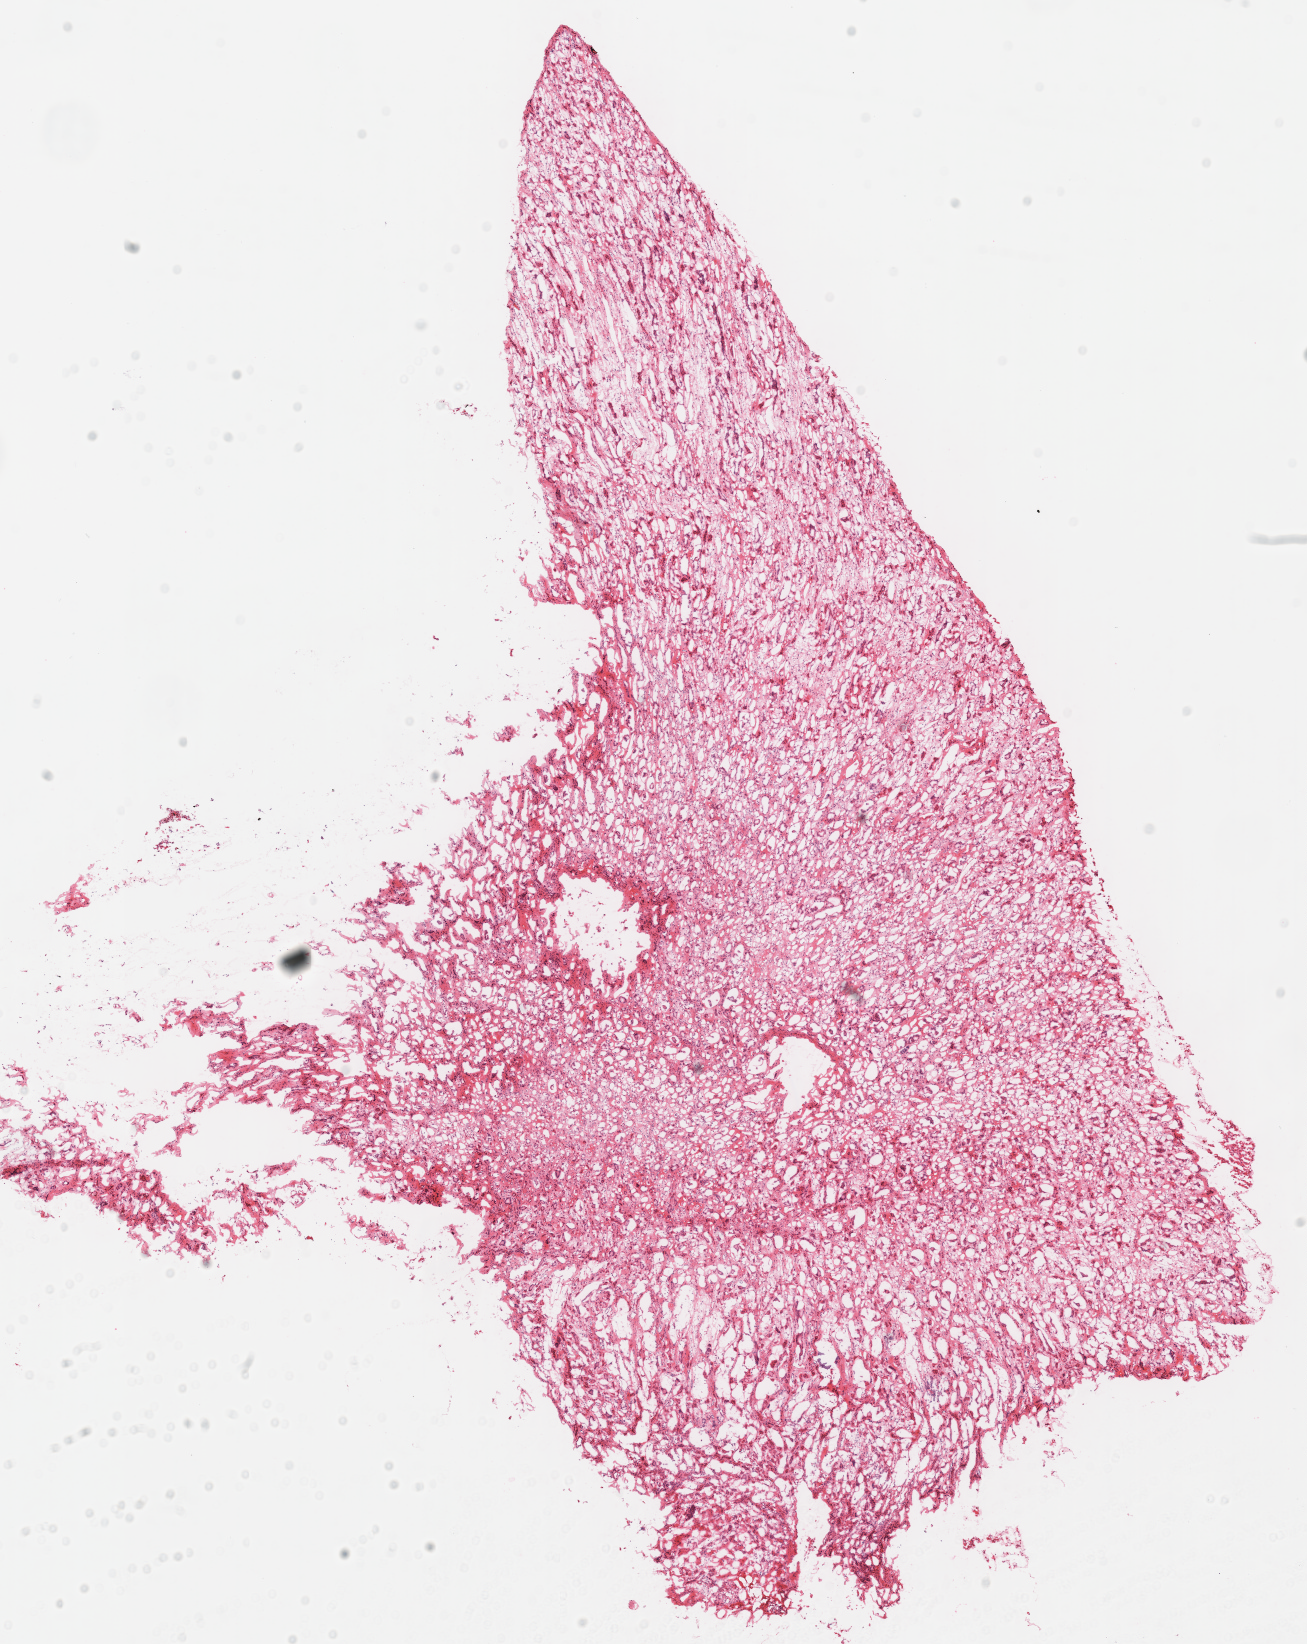
H&E whole-slide image — whole scanned area (about 10.3 x 12.9 mm) shown as a low-resolution overview, frozen section from the top of the tissue portion, sample: solid tissue normal (non-tumour tissue), kidney. Male patient; age at initial diagnosis 62 years. Inflammatory infiltration, as recorded: lymphocyte infiltration 0%, monocyte infiltration 0%, neutrophil infiltration 0%.
* this section: solid tissue normal (non-tumour) sample from the same patient
* patient diagnosis: Renal cell carcinoma, chromophobe type